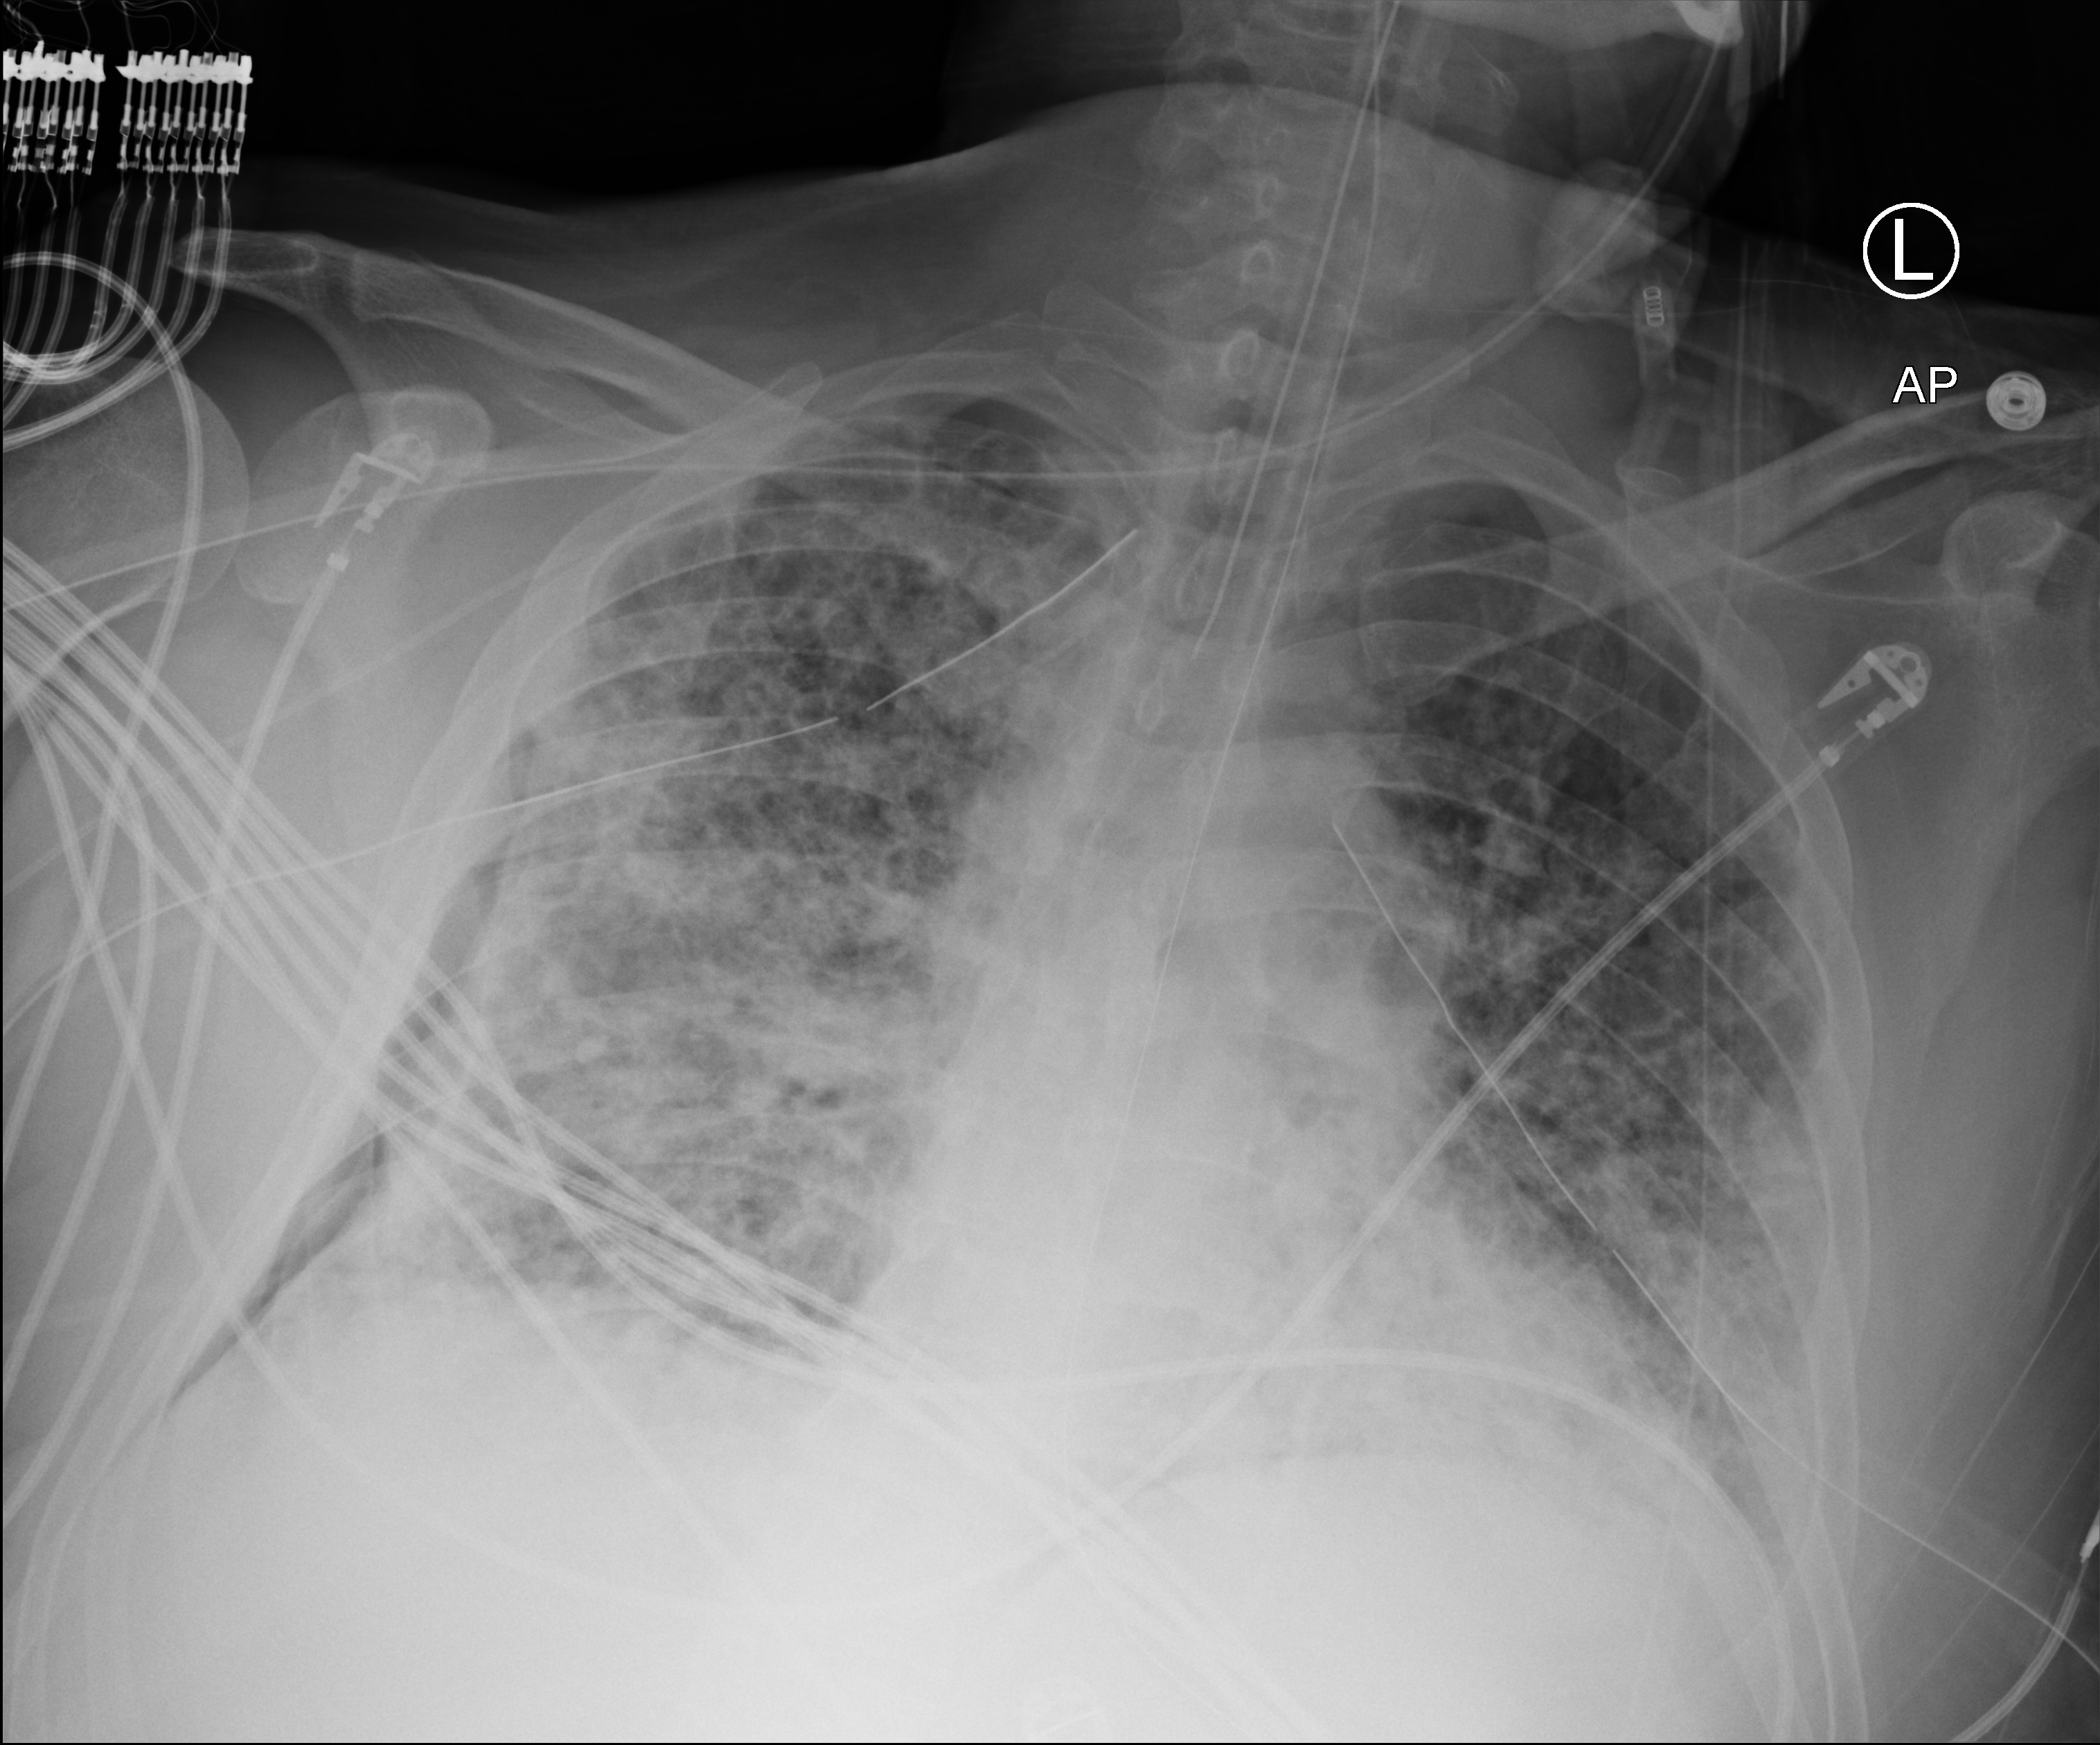
Chest X-ray (portable), anteroposterior (AP) projection. Male patient hospitalised with COVID-19, age 18–59 years.
Hospital-stay facts (about this admission, not read from this image; timing relative to this image not recorded): mechanically ventilated during this hospital stay: yes; smoking status (admission record): never.